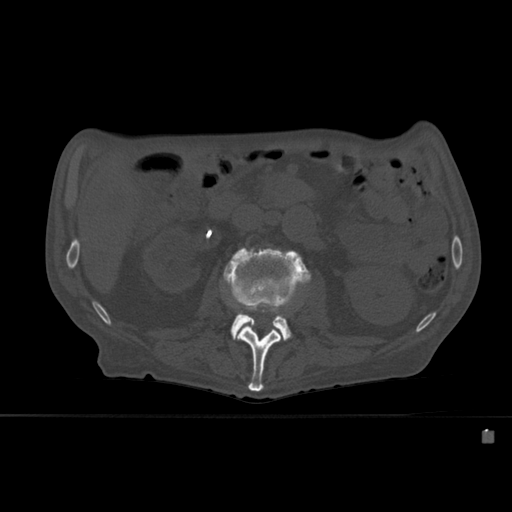
CT including the spine, one axial slice. Position 225 of 527 along the scan axis. Bone window (W 1800 / L 400 HU). 512 × 512 image matrix. Patient: male, 78 years. Case-level facts recorded for this patient, not image findings: primary cancer: prostate.
Annotated regions visible in this slice (semi-automatically segmented with operator editing):
- L2 vertebra: box from (x=227, y=291) to (x=308, y=392) px
- L3 vertebra: (x=223, y=247)–(x=311, y=341)